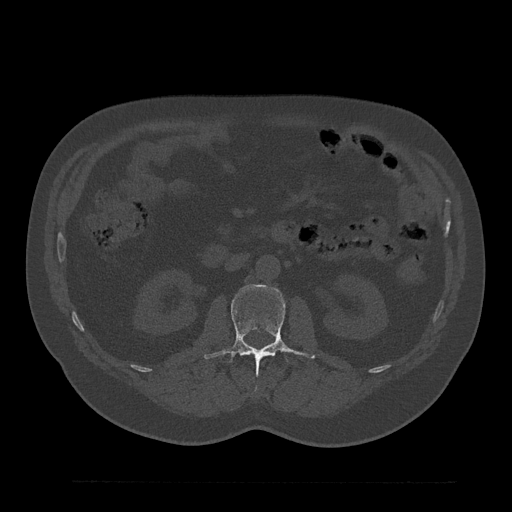
CT including the spine, one axial slice. Position 100 of 797 along the scan axis. 120 kVp. Bone window (W 1800 / L 400 HU). 512 × 512 image matrix, field of view 430 × 430 mm. Patient: male, 61 years. From the clinical record (not read from this slice): primary cancer: prostate.
Structures marked on this image (semi-automatically segmented with operator editing):
- L1 vertebra: box from (x=263, y=354) to (x=268, y=356) px
- L2 vertebra: (x=204, y=284)–(x=316, y=373)